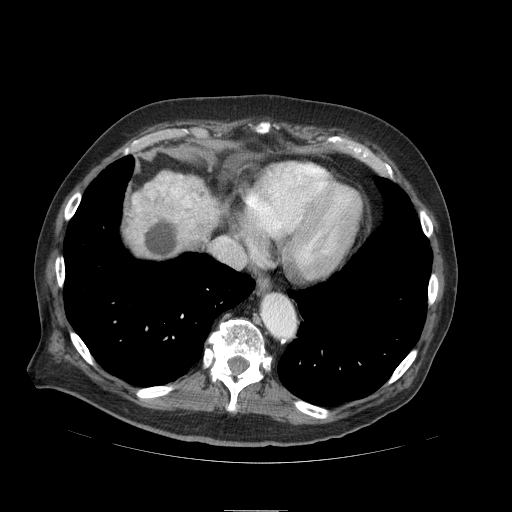
Contrast-enhanced abdominal CT (liver protocol), one axial slice. Position 83 of 103 along the scan axis. Soft-tissue window (W 400 / L 40 HU). 2.5 mm slice thickness. 512 × 512 image matrix, field of view 440 × 440 mm. From the clinical record (not read from this slice): diagnosis: hepatocellular carcinoma (patient treated with transarterial chemoembolisation; whether this scan precedes or follows treatment is not stated here); TNM stage (as recorded): Stage-IIIA; Child-Pugh class: B; tumour differentiation: well differentiated; tumour nodularity: multinodular.
Outlined on this slice (semi-automatically segmented with operator editing):
- liver parenchyma outside the tumour (the mass and vessels are separate outlines, so this box may not span the whole liver): bounding box [x1, y1, x2, y2] px = [126, 194, 178, 258]
- mass: [122, 169, 226, 255]